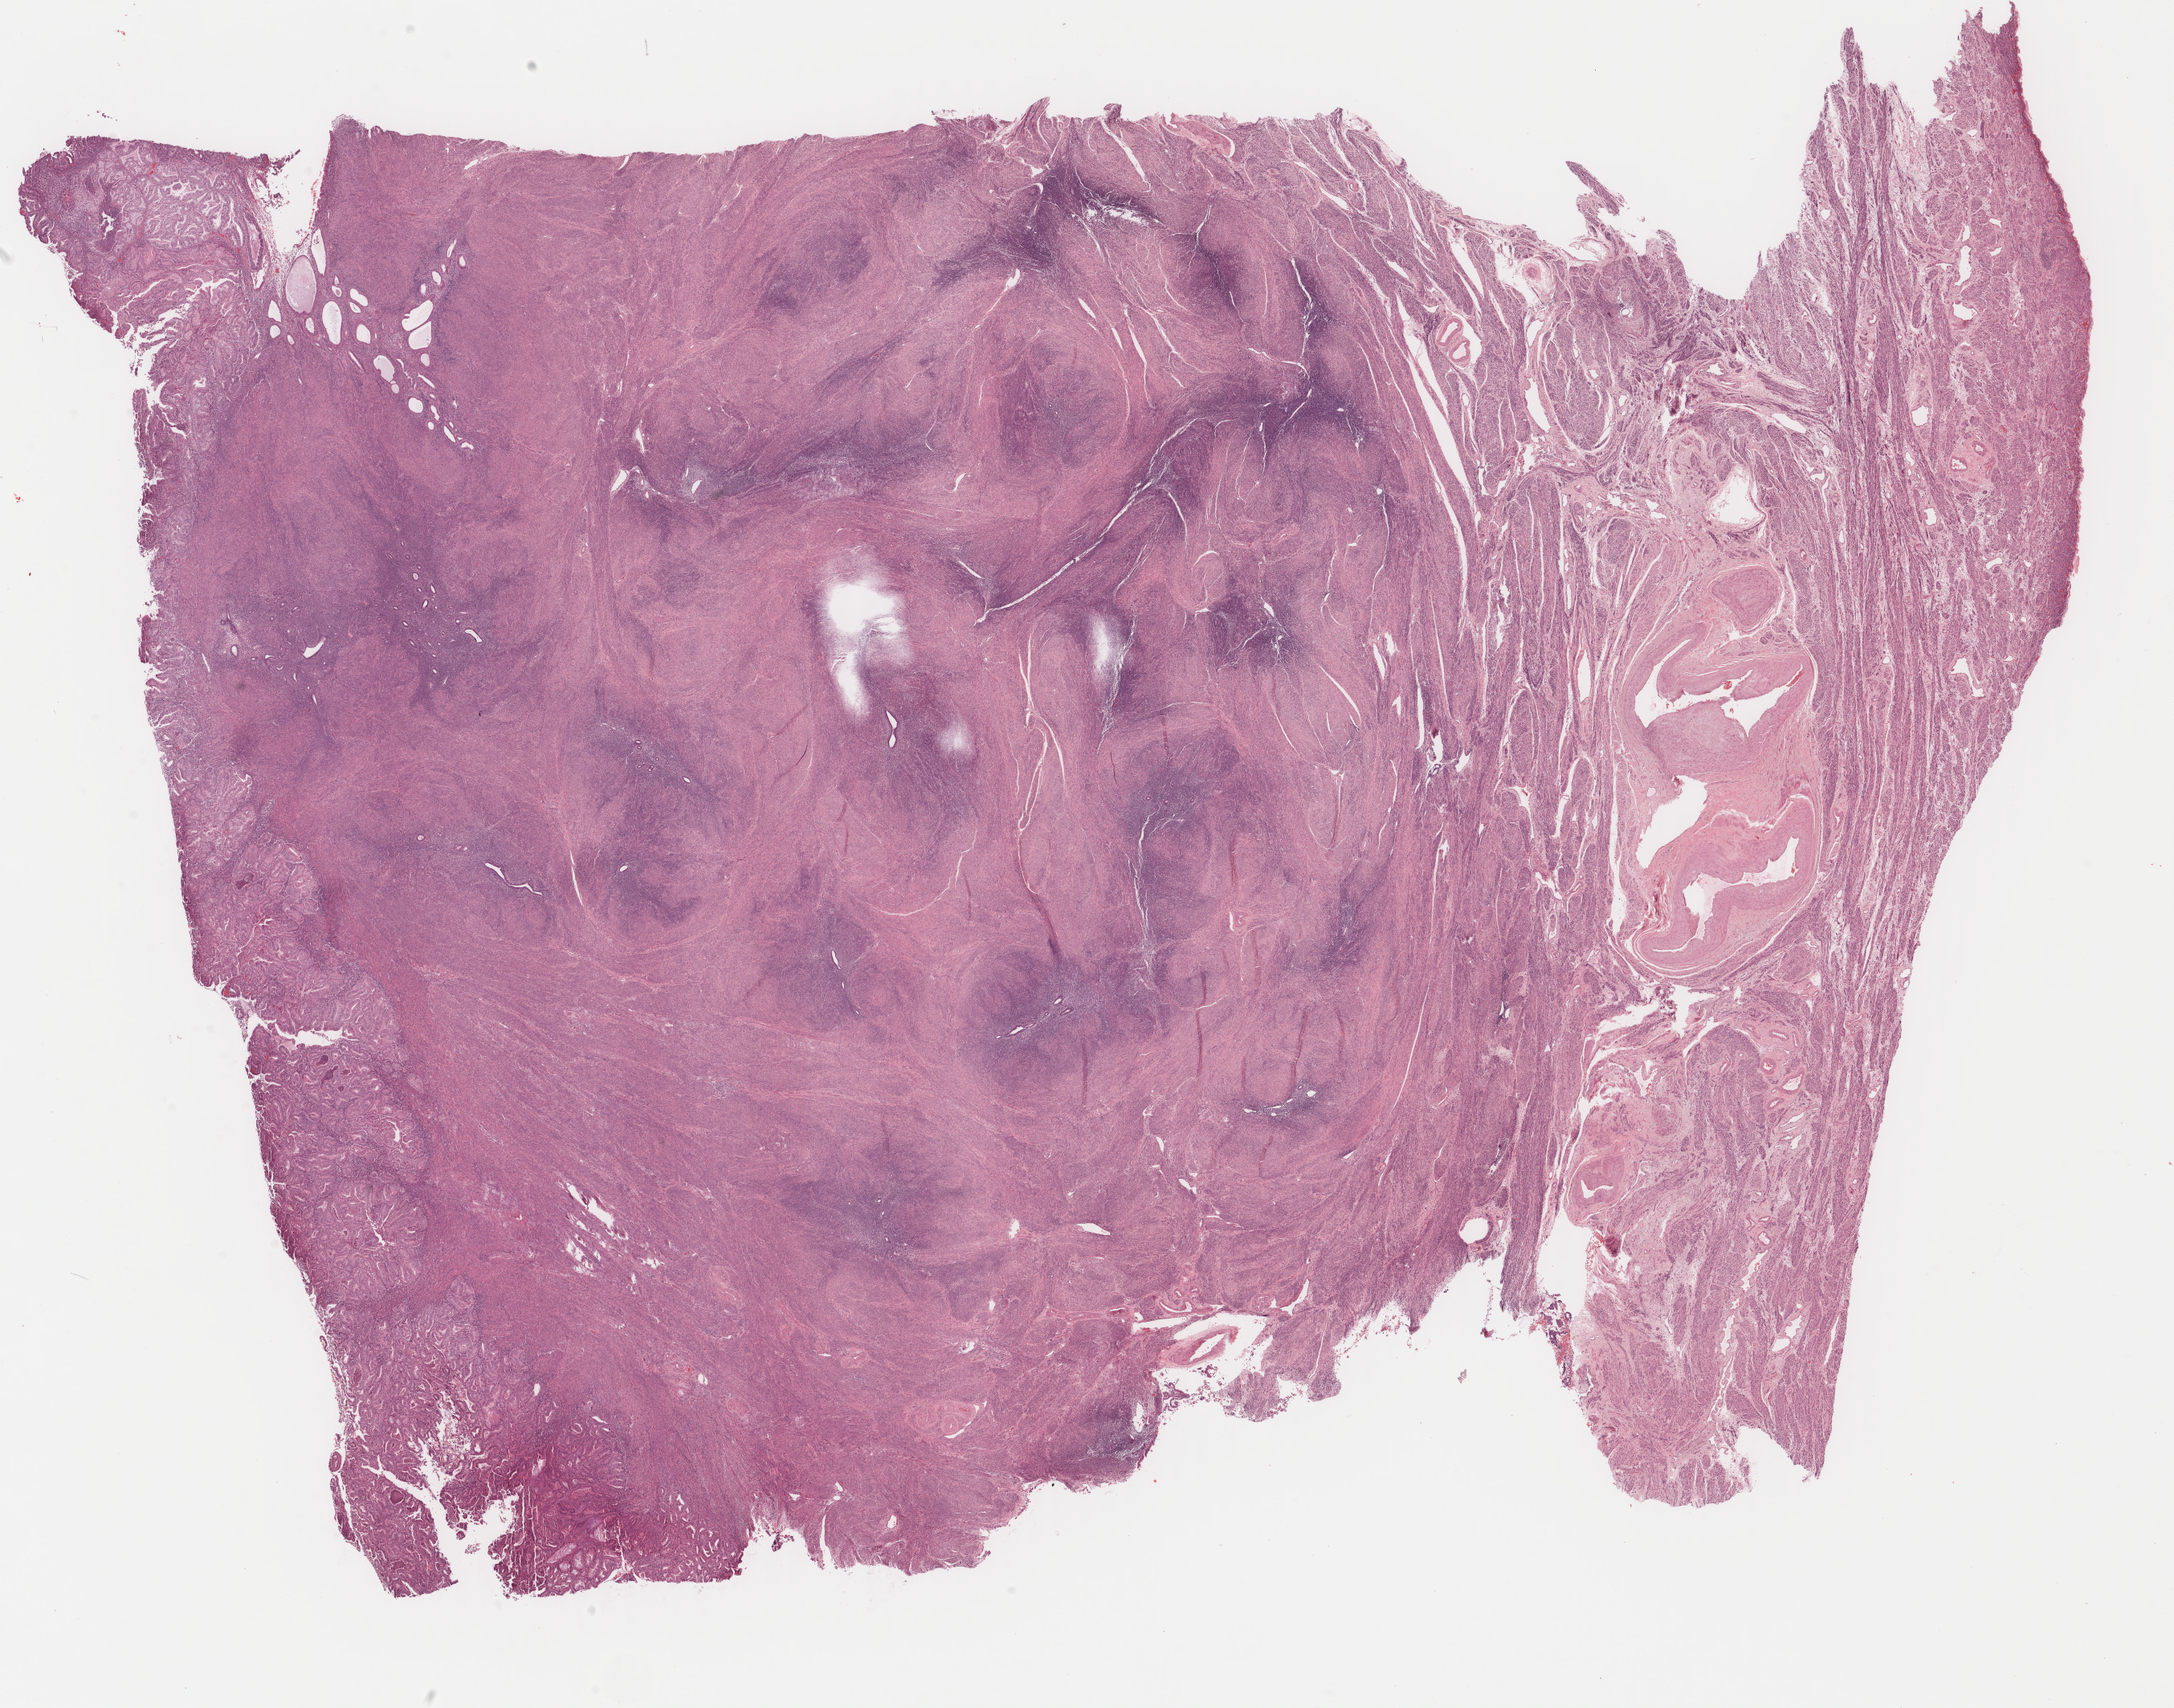
H&E whole-slide image, a low-resolution overview of the entire scanned area, about 21.5 x 16.9 mm (acquisition: 40x scan); formalin-fixed paraffin-embedded (FFPE) diagnostic section; primary tumour sample from the uterus. Female, age 68 years at initial diagnosis. Histologic grade: G1 (well differentiated).
Diagnosis: Endometrioid adenocarcinoma, NOS (endometrium). FIGO stage: IB.